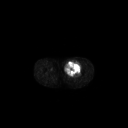
FDG PET of an extremity soft-tissue mass (from a PET/CT study), one axial slice. Position 242 of 267 along the scan axis. 128 × 128 image matrix, field of view 700 × 700 mm. Male patient, age 63 years. From the clinical record (not read from this slice): histological type: pleiomorphic liposarcoma; grade: high; site of the primary tumour: left thigh.
Annotated regions visible in this slice (expert contour drawn on MRI and transferred to this co-registered scan by the dataset authors):
- gross tumour volume including surrounding oedema: bounding box <65,60,82,76> (left, top, right, bottom; pixels)
- gross tumour volume (mass): <65,60,81,76>